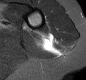
MRI of an extremity soft-tissue mass, one axial slice. Position 5 of 30 along the scan axis. STIR. MR volume resampled by the dataset authors to the PET/CT grid (not the native acquisition matrix). 86 × 80 image matrix, field of view 84 × 78 mm. Female patient. Case-level facts recorded for this patient, not image findings: histological type: malignant fibrous histiocytoma; grade: low; site of the primary tumour: left arm.
Structures marked on this image (expert contour drawn on MRI and transferred to this co-registered scan by the dataset authors):
- gross tumour volume (mass): bounding box [x1, y1, x2, y2] px = [35, 35, 54, 52]